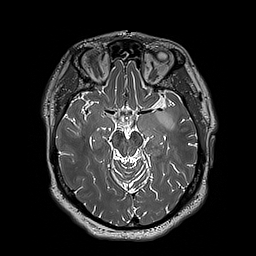
Brain MRI from a brain-tumour surgery series, one axial slice; slice 119 of 192 in the series (ordered by position); 1 mm slice thickness; 256 × 256 image matrix, field of view 250 × 250 mm. From the clinical record (not read from this slice): histopathology: Astrocytoma; WHO grade: 3; IDH mutation: yes; tumour location: Left Insular.
Outlined on this slice (manually delineated by an expert):
- tumour: bounding box <153,105,175,130> (left, top, right, bottom; pixels)